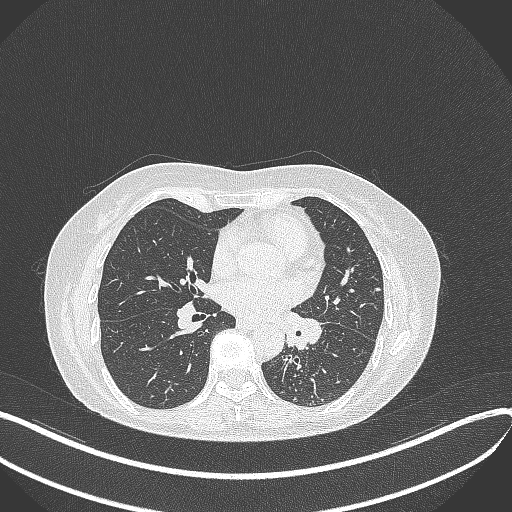
Chest CT, one axial slice; position 198 of 429 along the scan axis; reconstruction kernel B70f; 100 kVp; lung window (W 1500 / L -600 HU); 1 mm slice thickness; 512 × 512 image matrix, field of view 400 × 400 mm. Patient: female, 63 years. Case-level facts recorded for this patient, not image findings: clinical TNM (as recorded): T1b N0 M0; histopathological grade: G2-3.
Outlined on this slice (bounding box drawn by a radiologist):
- lung tumour (recorded histology: adenocarcinoma): bounding box [x1, y1, x2, y2] px = [277, 308, 325, 353]